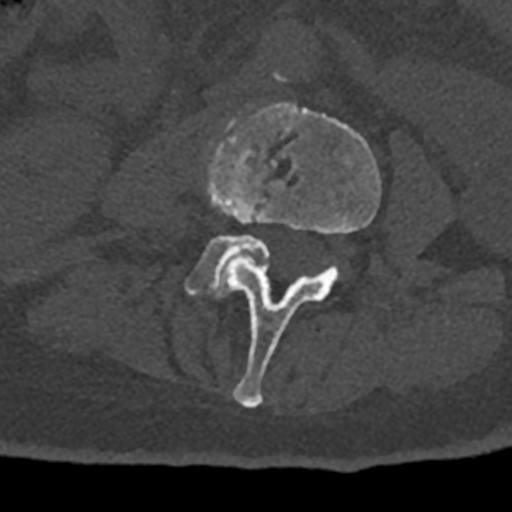
CT including the spine, one axial slice; position 302 of 797 along the scan axis; 120 kVp; bone window (W 1800 / L 400 HU); 0.5 mm slice thickness; 512 × 512 image matrix. Patient: male, 74 years. Case-level facts recorded for this patient, not image findings: primary cancer: renal; vertebrae with lytic lesions (as recorded): T10, L1, L2, L3, L4, L5.
Structures marked on this image (semi-automatically segmented with operator editing):
- L3 vertebra: box from (x=205, y=104) to (x=381, y=408) px
- L4 vertebra: (x=185, y=234)–(x=270, y=297)